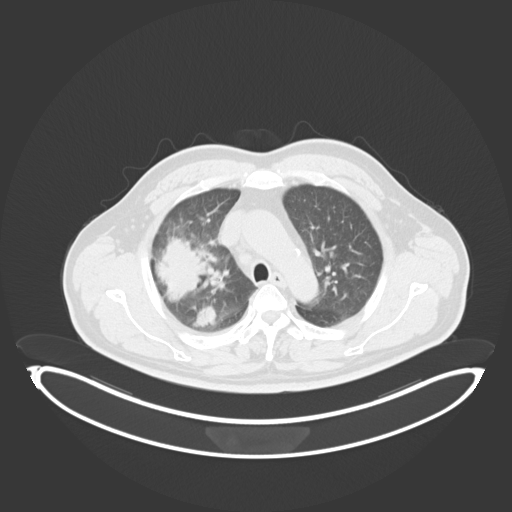
Chest CT, one axial slice; slice 223 of 284 in the series (ordered by position); reconstruction kernel B30f; 120 kVp; lung window (W 1500 / L -600 HU); 512 × 512 image matrix, field of view 500 × 500 mm. Patient: male, 55 years. From the clinical record (not read from this slice): clinical TNM (as recorded): T3 N2 M1.
Outlined on this slice (bounding box drawn by a radiologist):
- lung tumour (recorded histology: adenocarcinoma): bounding box (x1, y1, x2, y2) in pixels: (154, 229, 209, 300)